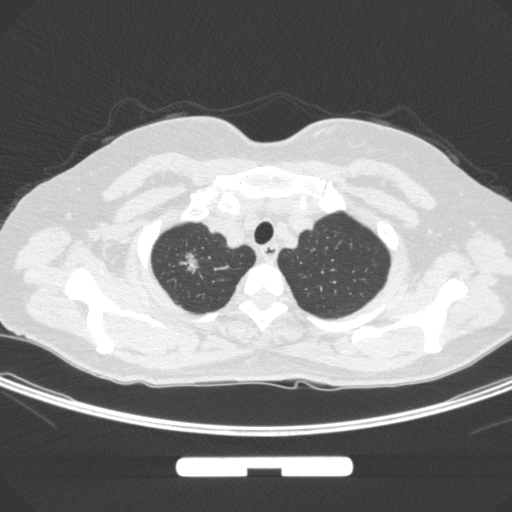
Chest CT, one axial slice; slice 259 of 295 in the series (ordered by position); lung window (W 1500 / L -600 HU); 1 mm slice thickness; 512 × 512 image matrix, field of view 369 × 369 mm. Patient: female, 58 years. Case-level facts recorded for this patient, not image findings: clinical TNM (as recorded): T1b N0 M0.
Structures marked on this image (bounding box drawn by a radiologist):
- lung tumour (recorded histology: adenocarcinoma): box from (x=172, y=245) to (x=201, y=280) px